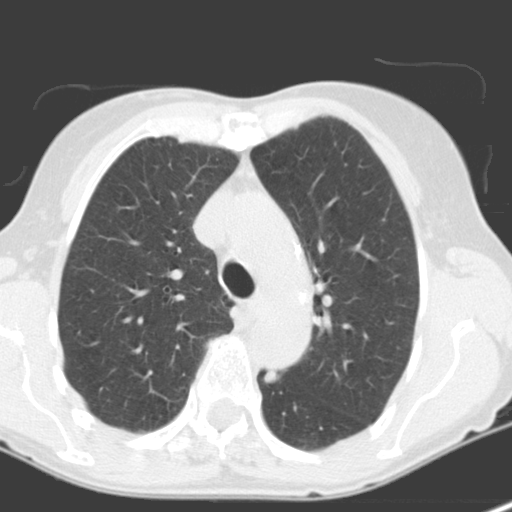
Low-dose screening chest CT, one axial slice. Position 104 of 141 along the scan axis. 120 kVp. Lung window (W 1500 / L -600 HU). 3.2 mm slice thickness. 512 × 512 image matrix, field of view 262 × 262 mm.
Structures marked on this image (outlined manually by an expert reader):
- lesion 1 (tumor, lower lobe of left lung): box from (x=265, y=371) to (x=280, y=384) px